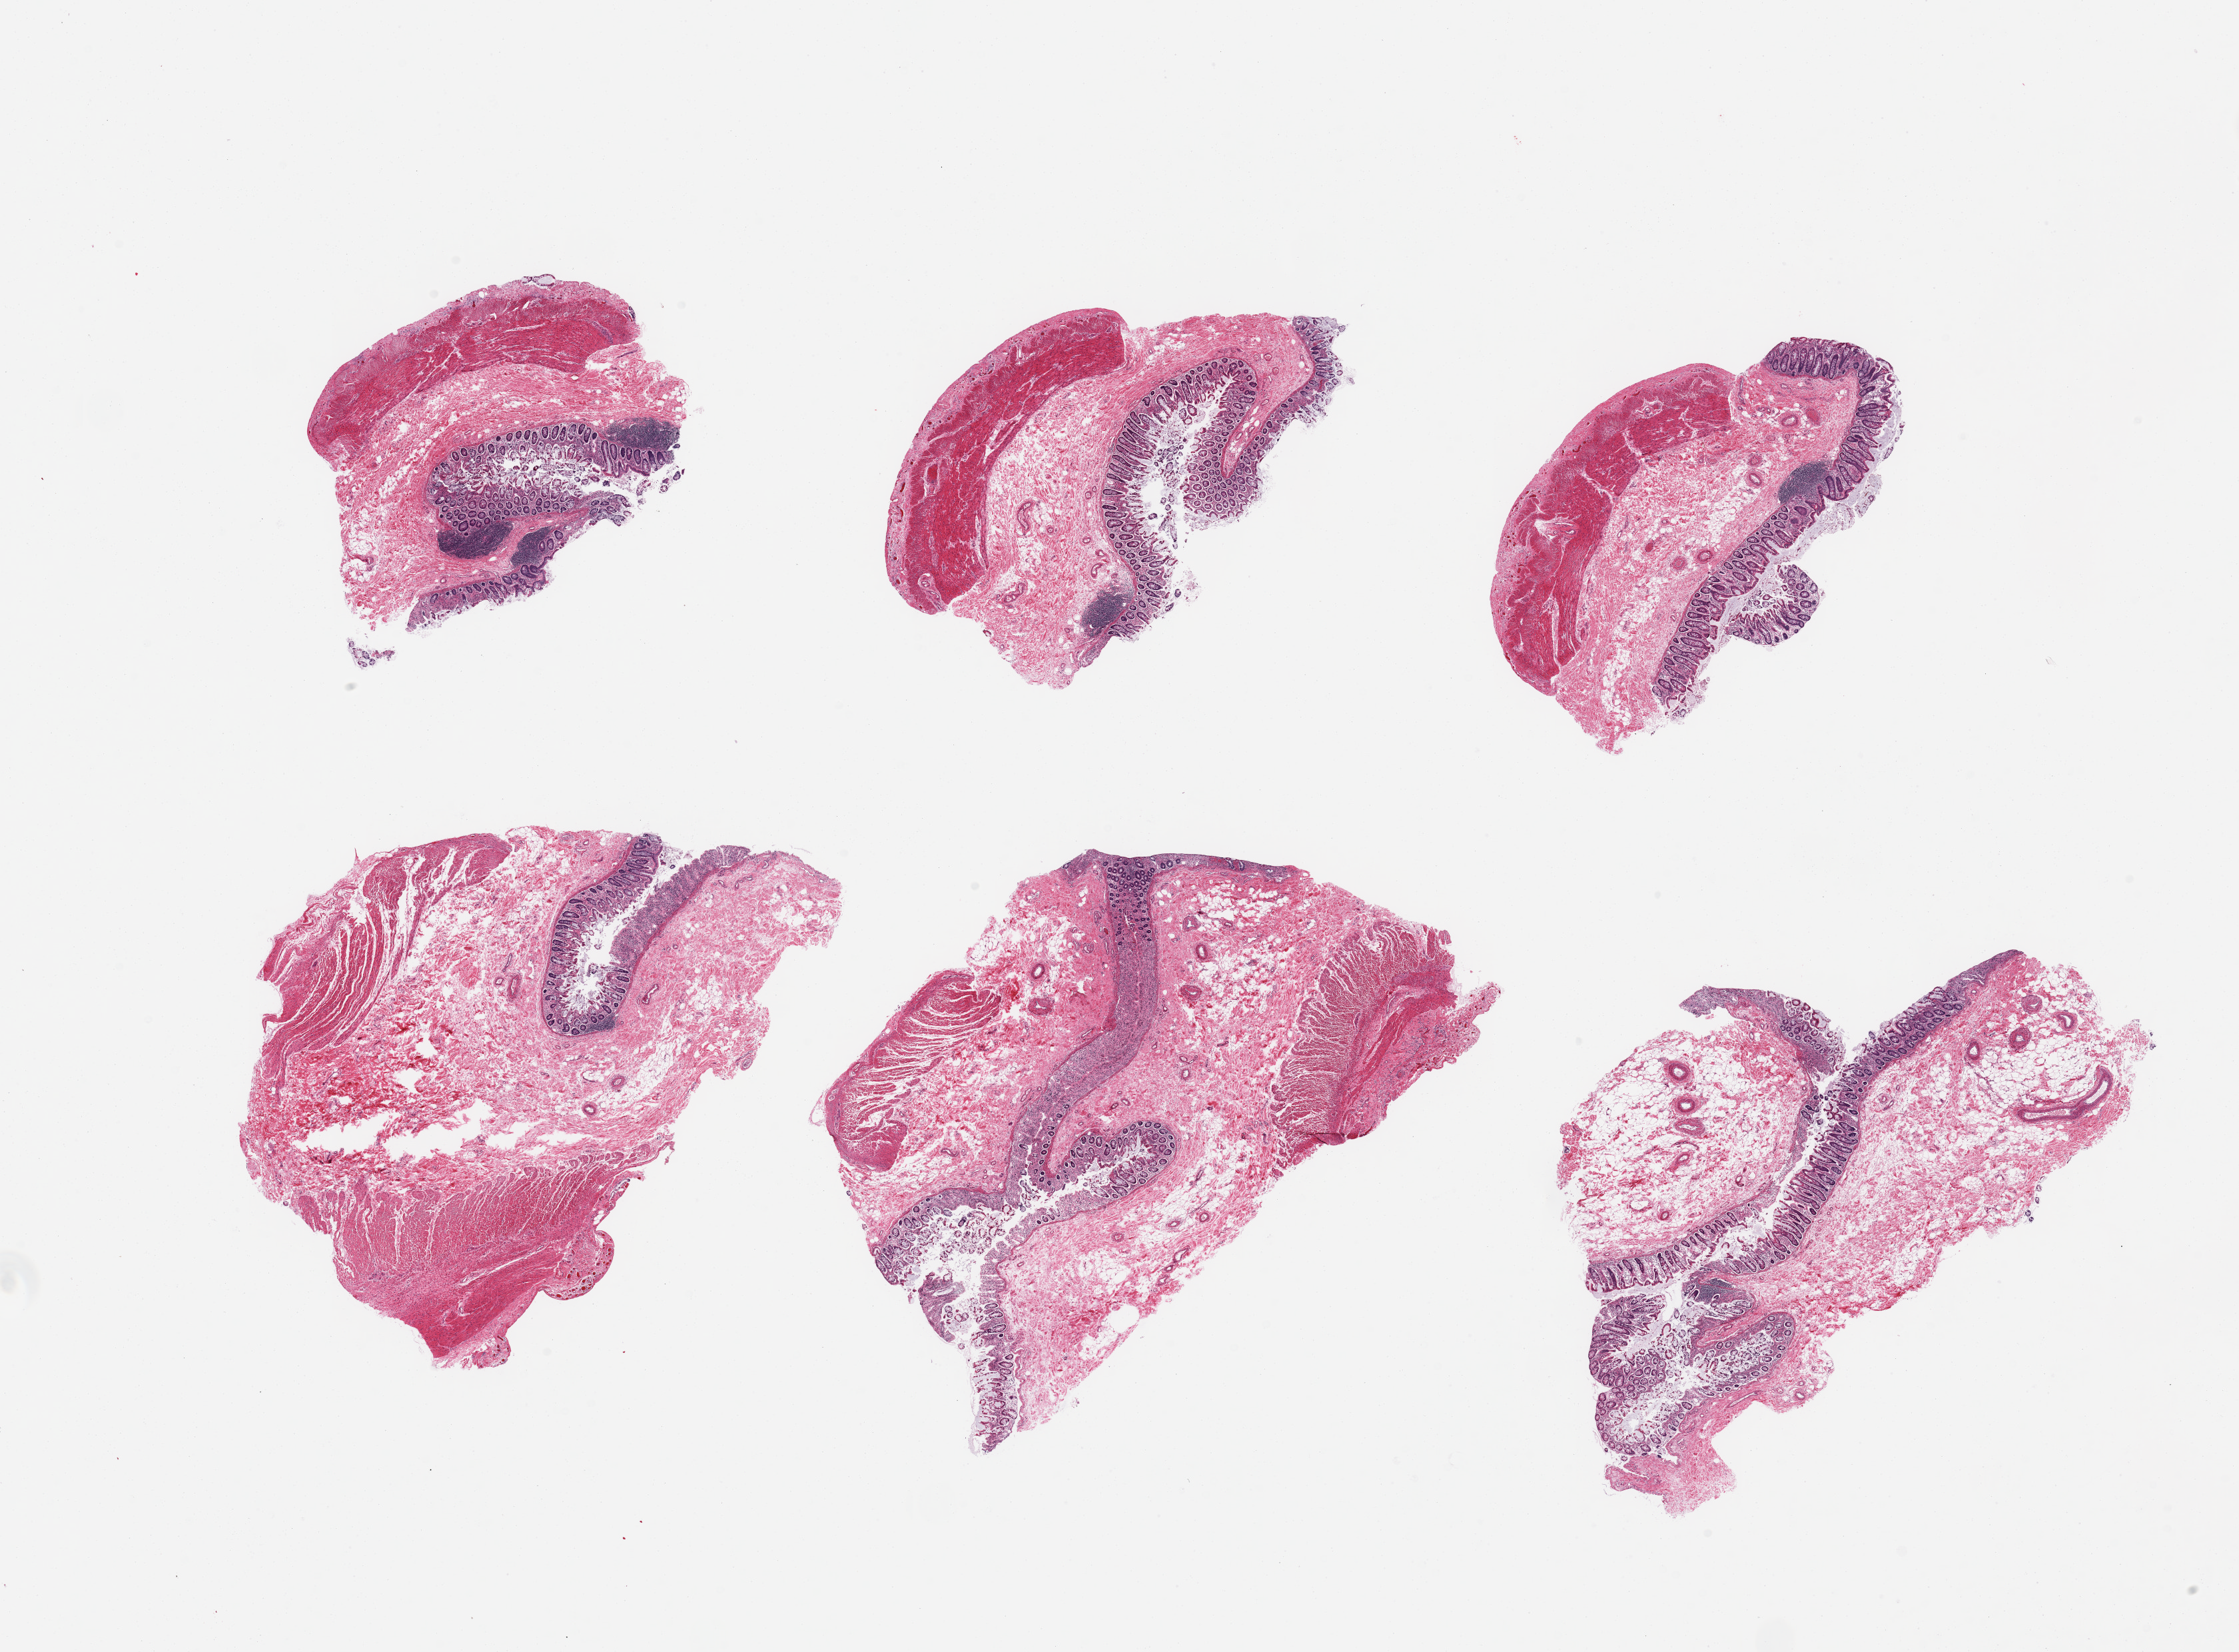
Hematoxylin and eosin (H&E) whole-slide image, a low-resolution overview of the entire scanned area, about 26.6 x 19.6 mm, PAXgene-fixed, paraffin-embedded tissue, section of ileum (target tissue), donor tissue sample.
• review note (as recorded): 6 pieces; colonic mucosa and wall